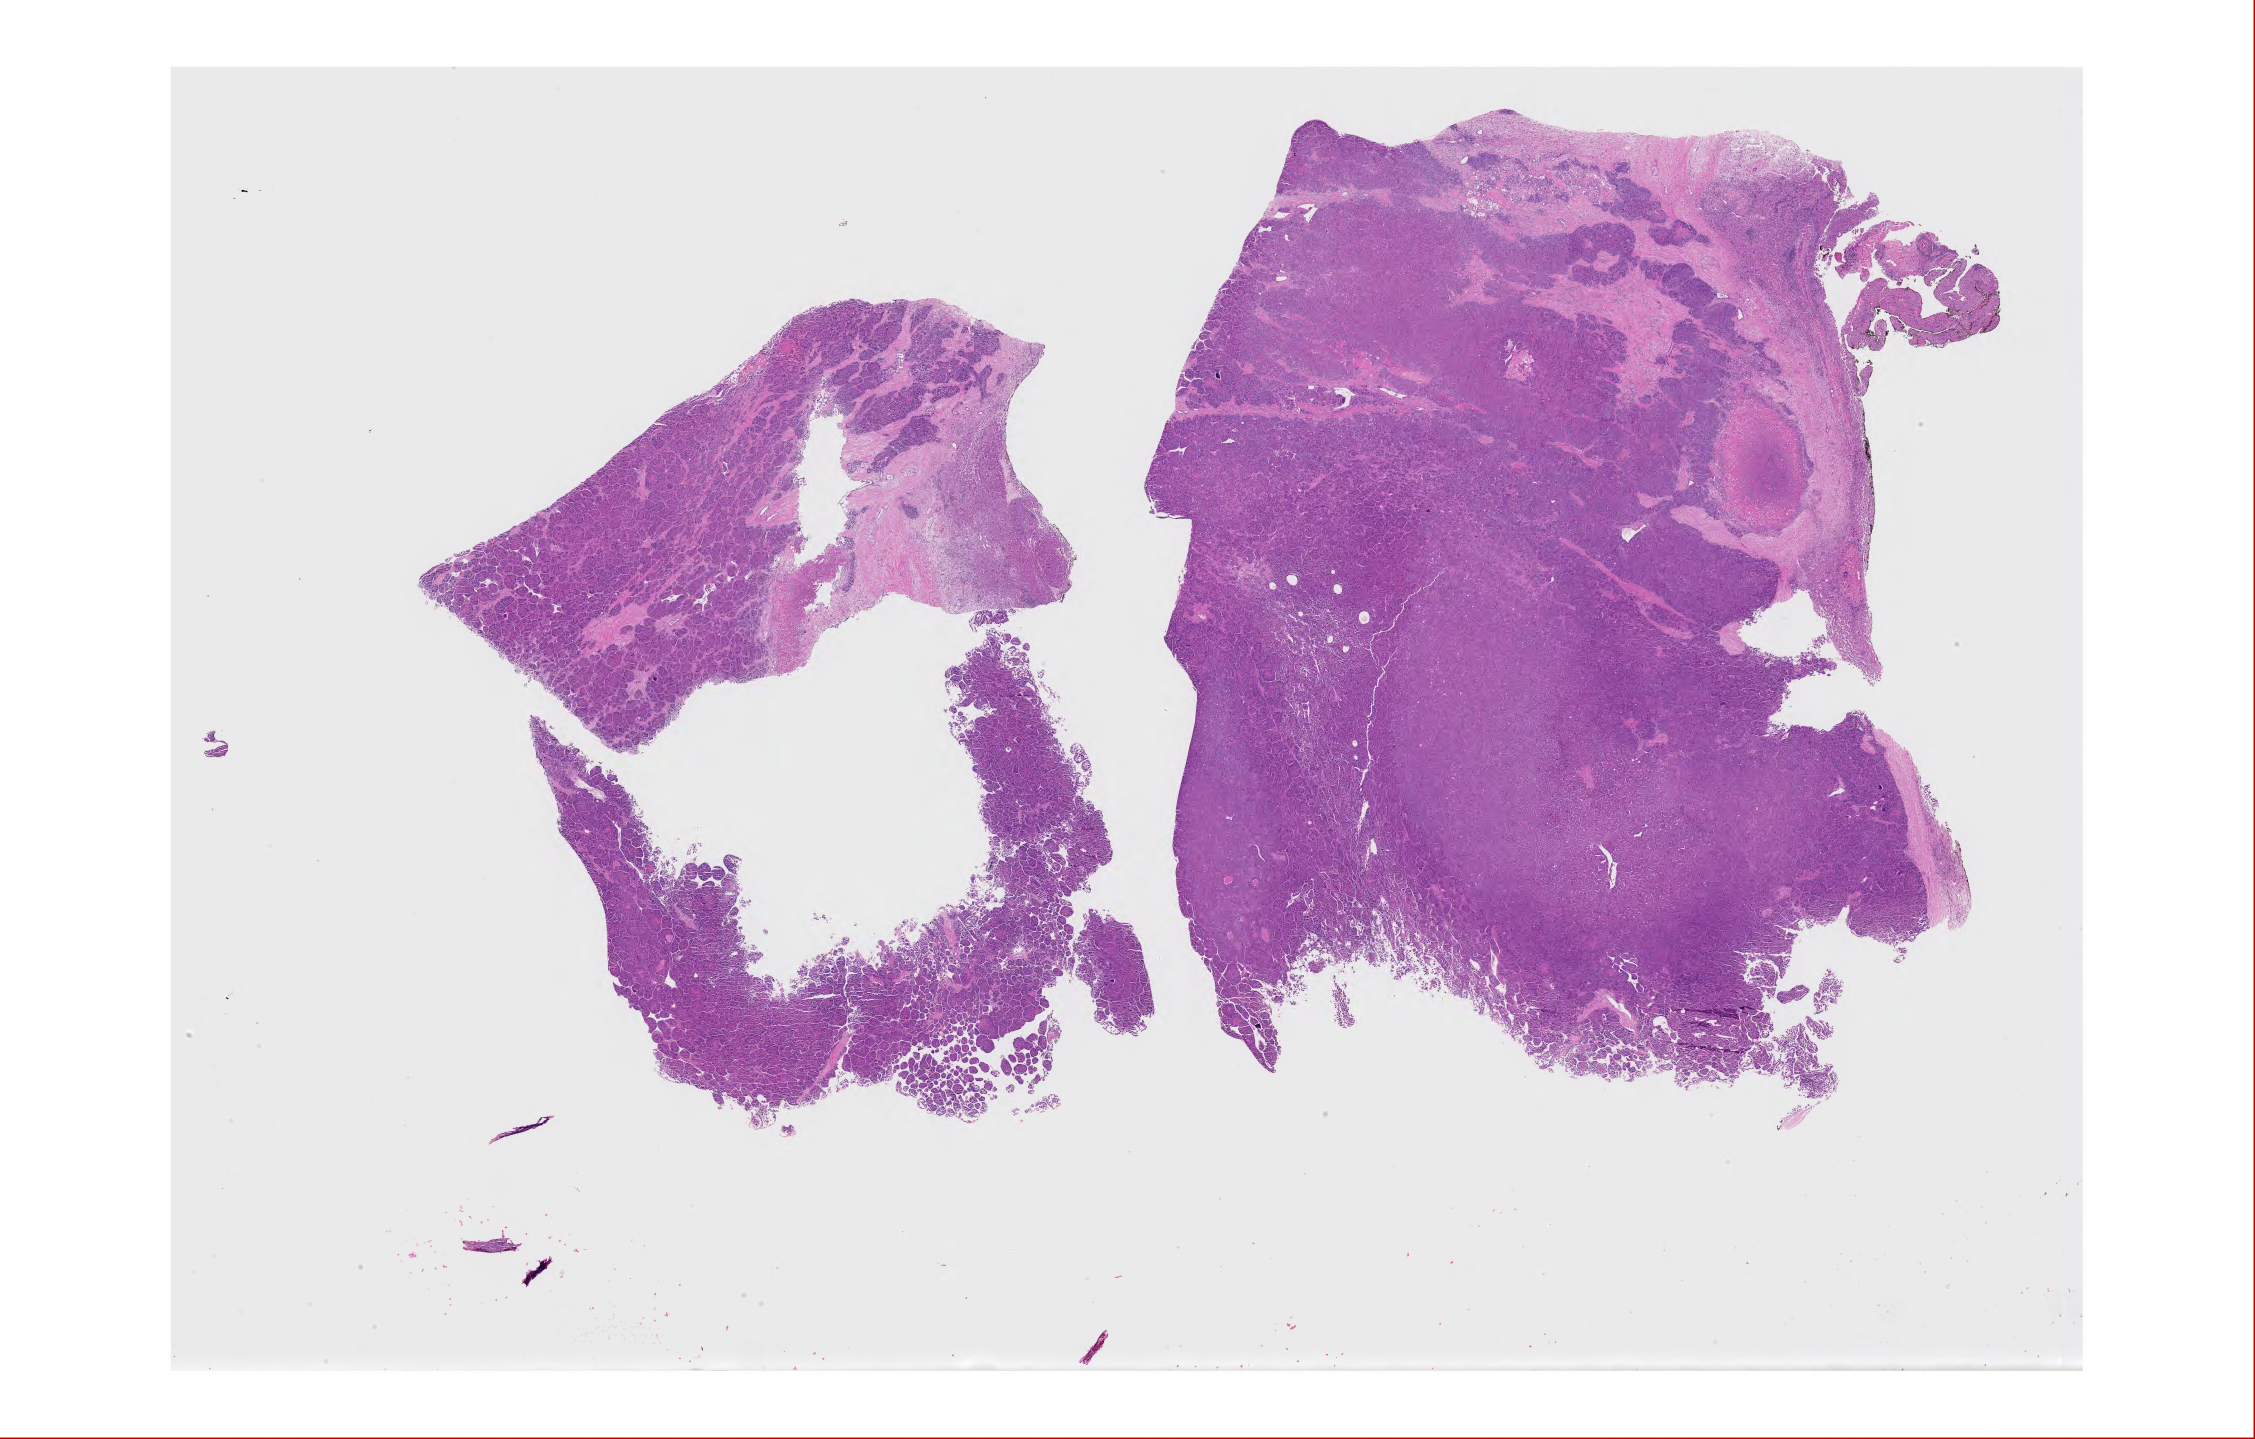
H&E whole-slide image, whole scanned area (about 36.1 x 23.0 mm, acquisition: 20x scan) shown as a low-resolution overview; FFPE section; liver, primary tumour sample. Patient: female, age at initial diagnosis 73 years. Histologic grade: G3 (poorly differentiated).
- histologic diagnosis: Hepatocellular carcinoma, NOS
- AJCC pathologic stage: I (6th edition)